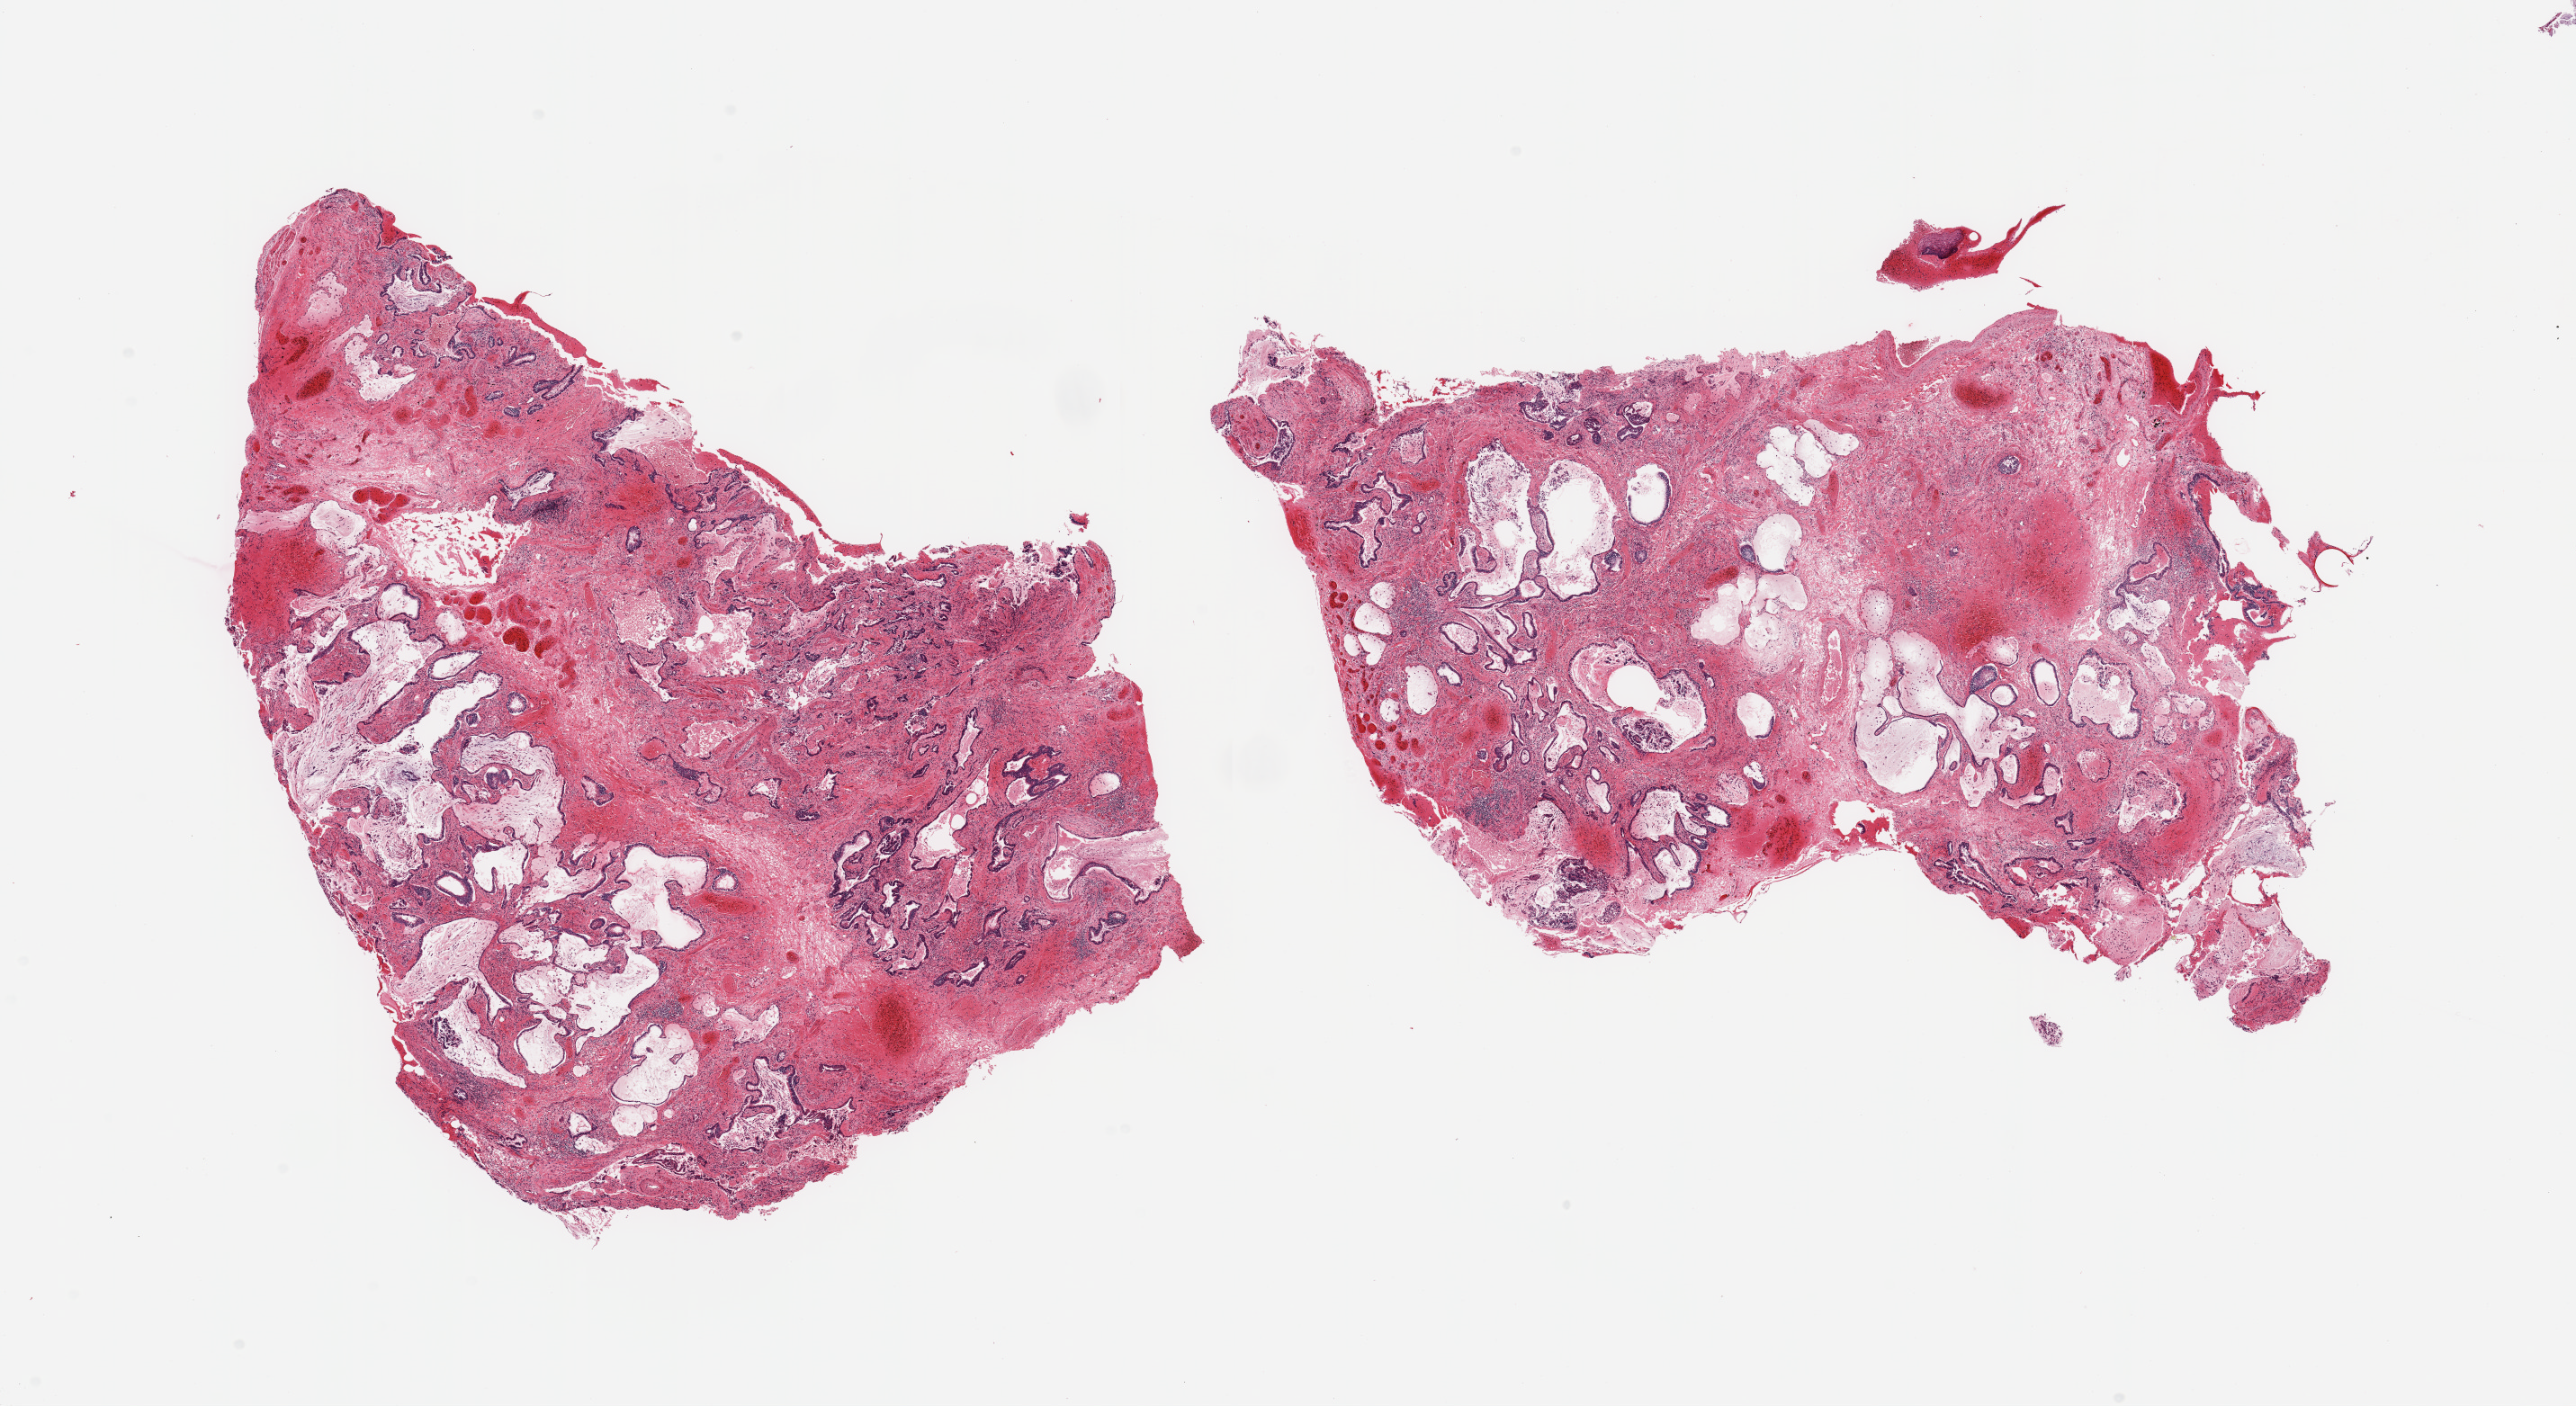
Whole-slide image, hematoxylin and eosin (H&E) stain — whole scanned area (about 22.6 x 12.4 mm, slide scanned at 20x) shown as a low-resolution overview; PAXgene-fixed, paraffin-embedded tissue; section of lung (target tissue); tissue donor sample. Donor sex: male.
Pathologist's review note for this sample: 2 pieces, end-stage fibrosing pneumontiis.